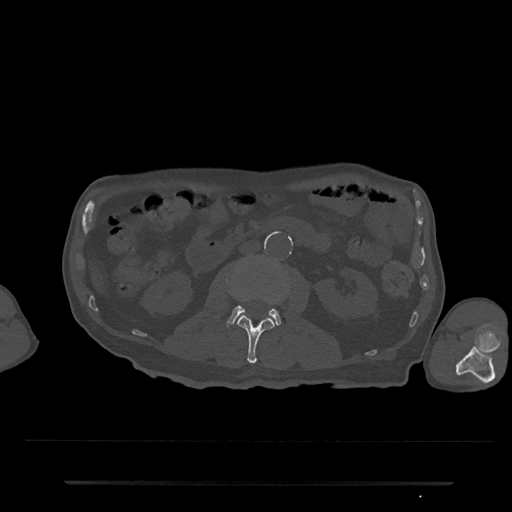
CT including the spine, one axial slice. Slice 30 of 797 in the series (ordered by position). Reconstruction kernel Br40s/3. Bone window (W 1800 / L 400 HU). 0.5 mm slice thickness. 512 × 512 image matrix. Patient: male, 74 years. Case-level facts recorded for this patient, not image findings: primary cancer: prostate.
Annotated regions visible in this slice (semi-automatic segmentation, software-assisted and operator-edited):
- L2 vertebra: box from (x=237, y=299) to (x=281, y=364) px
- L3 vertebra: (x=226, y=305)–(x=282, y=328)